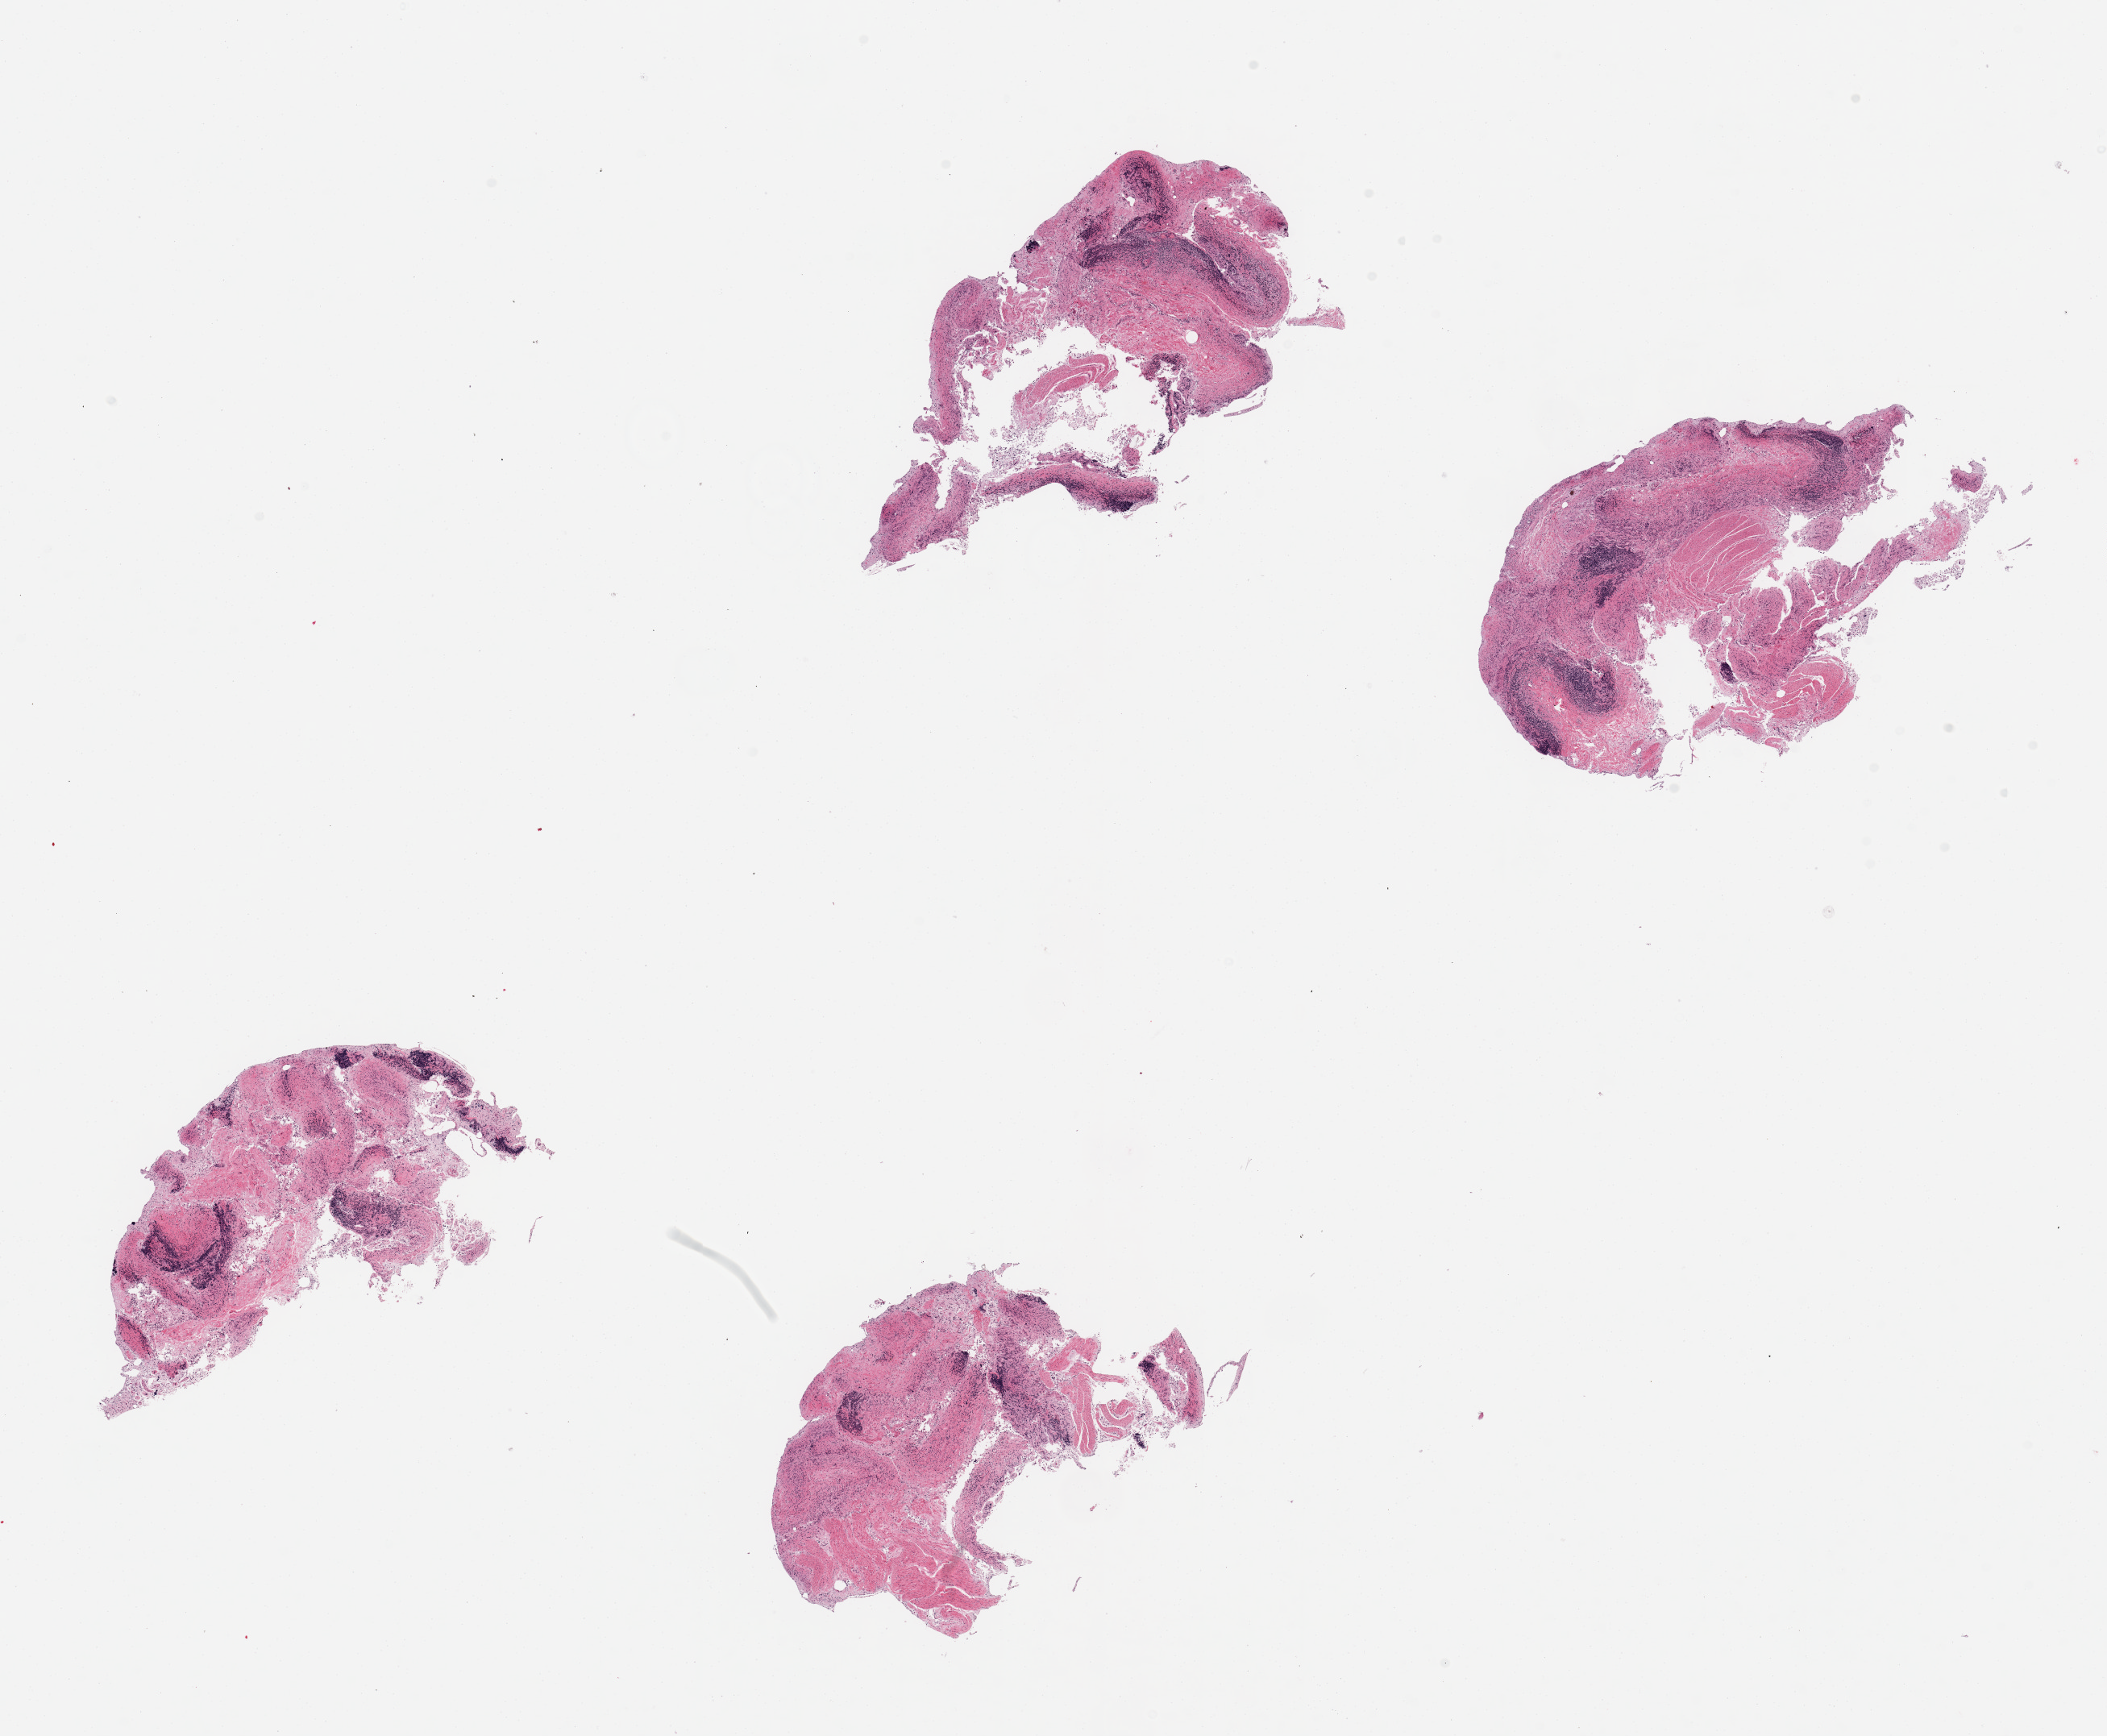
Digitized haematoxylin and eosin-stained section — low-resolution overview of the scanned area, about 20.7 x 17.0 mm (from a 20x scan). Male donor.
Specimen: PAXgene-fixed paraffin-embedded (PFPE) section; target tissue: ileum; donor tissue sample.